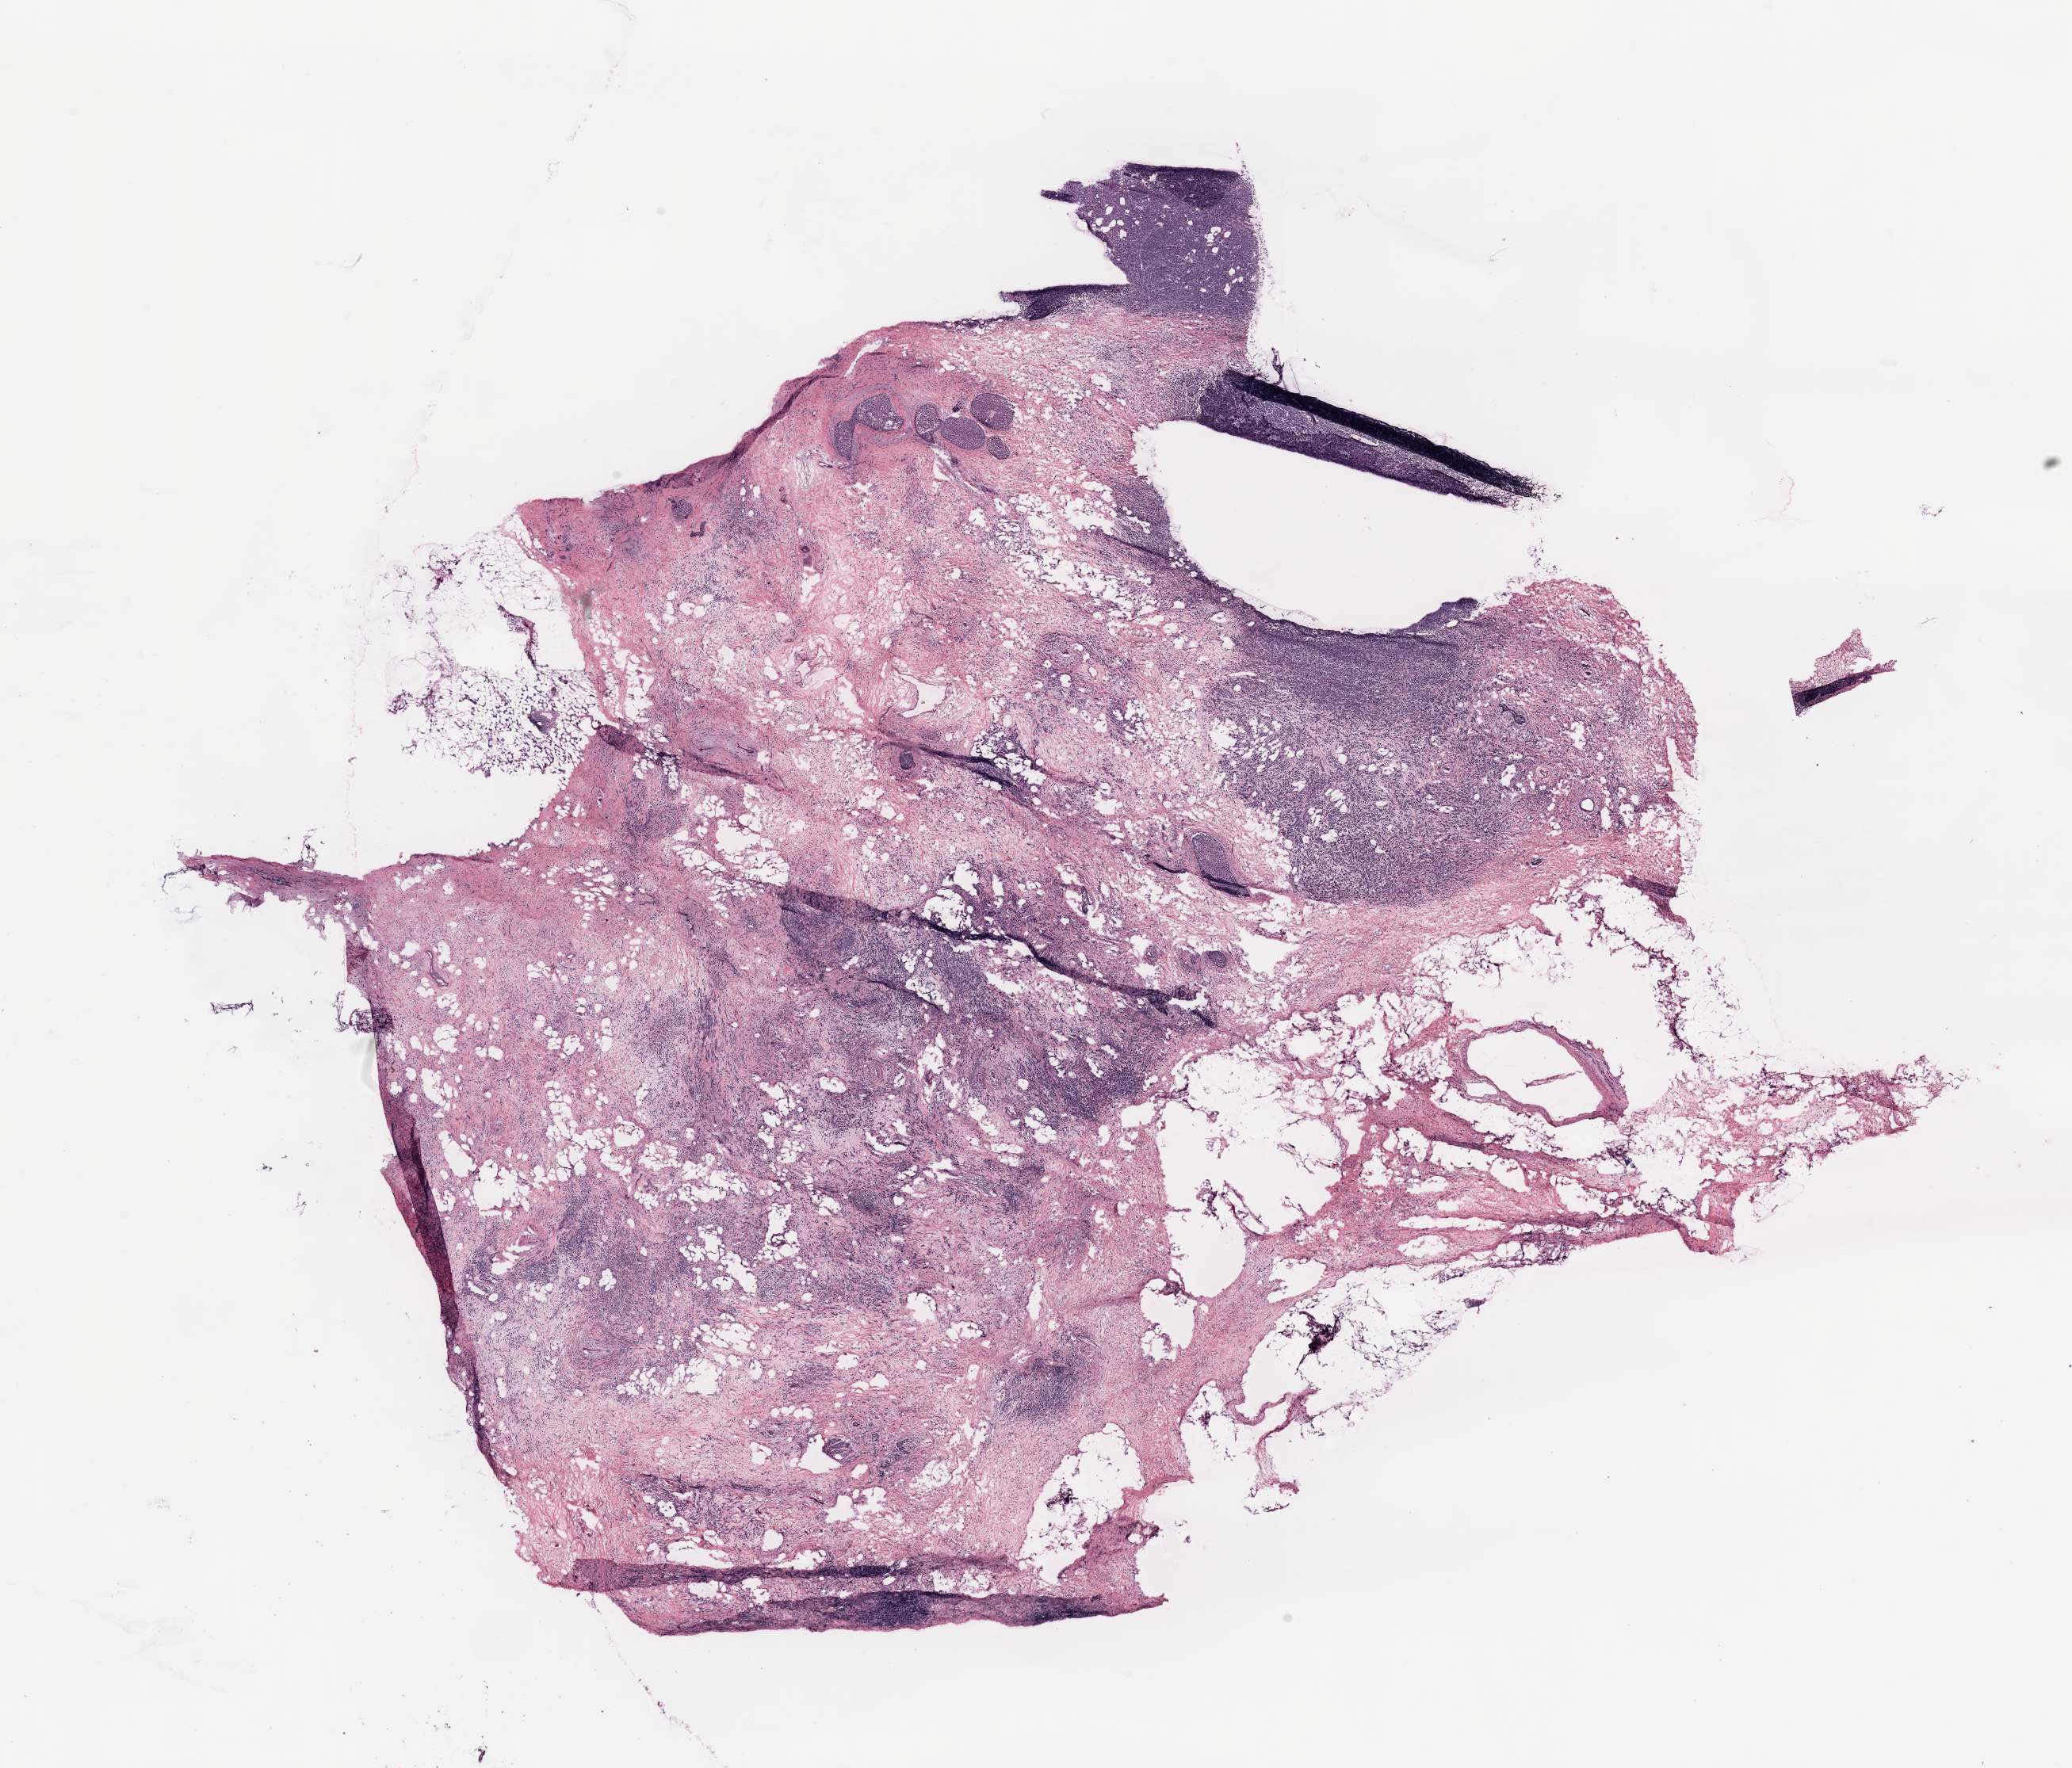
Whole-slide histology image, H&E-stained — whole scanned area (about 20.7 x 17.6 mm) shown as a low-resolution overview. Breast, tumour tissue. Female, 70 y/o.
Diagnosis: Infiltrating lobular carcinoma, NOS. AJCC pathologic stage: IIA.